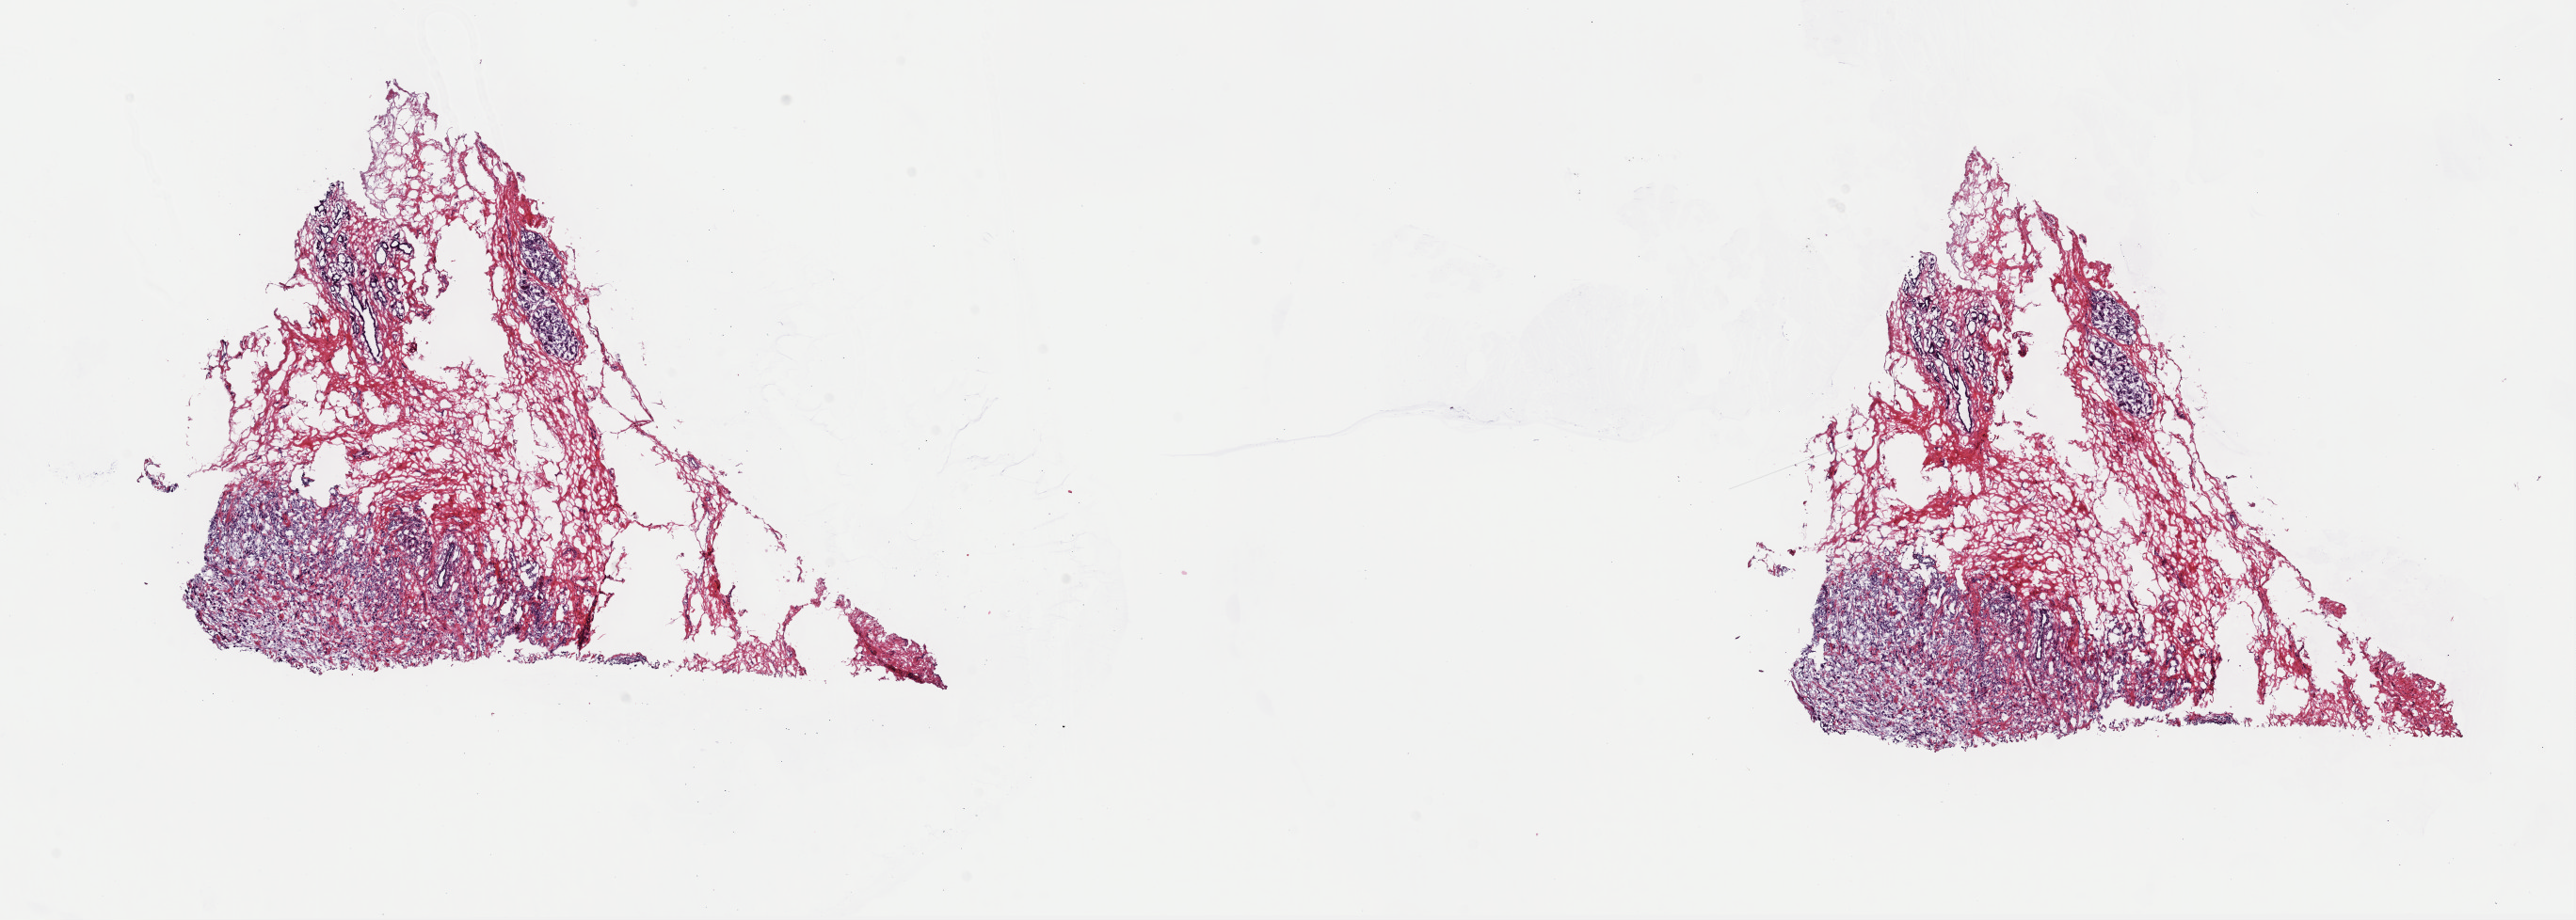
Digitized Hematoxylin and eosin (H&E) stained tissue section (whole slide) — shown as a low-resolution overview of the whole scanned area (about 21.6 x 7.7 mm, acquisition: 40x scan); frozen section; sample: primary tumour, breast. Female, age 44 years at initial diagnosis. Pathologist review of this section (percent, as recorded): tumour cells 30%, tumour nuclei 65%, normal cells 20%, stromal cells 50%, necrosis 0%. Infiltration values recorded for this section: lymphocyte infiltration 1%, monocyte infiltration 0%, neutrophil infiltration 0%.
Laterality: left. AJCC pathologic stage: IIB. Lymph nodes positive (case pathology): 2 of 18 examined. Pathologic diagnosis: Lobular carcinoma, NOS.